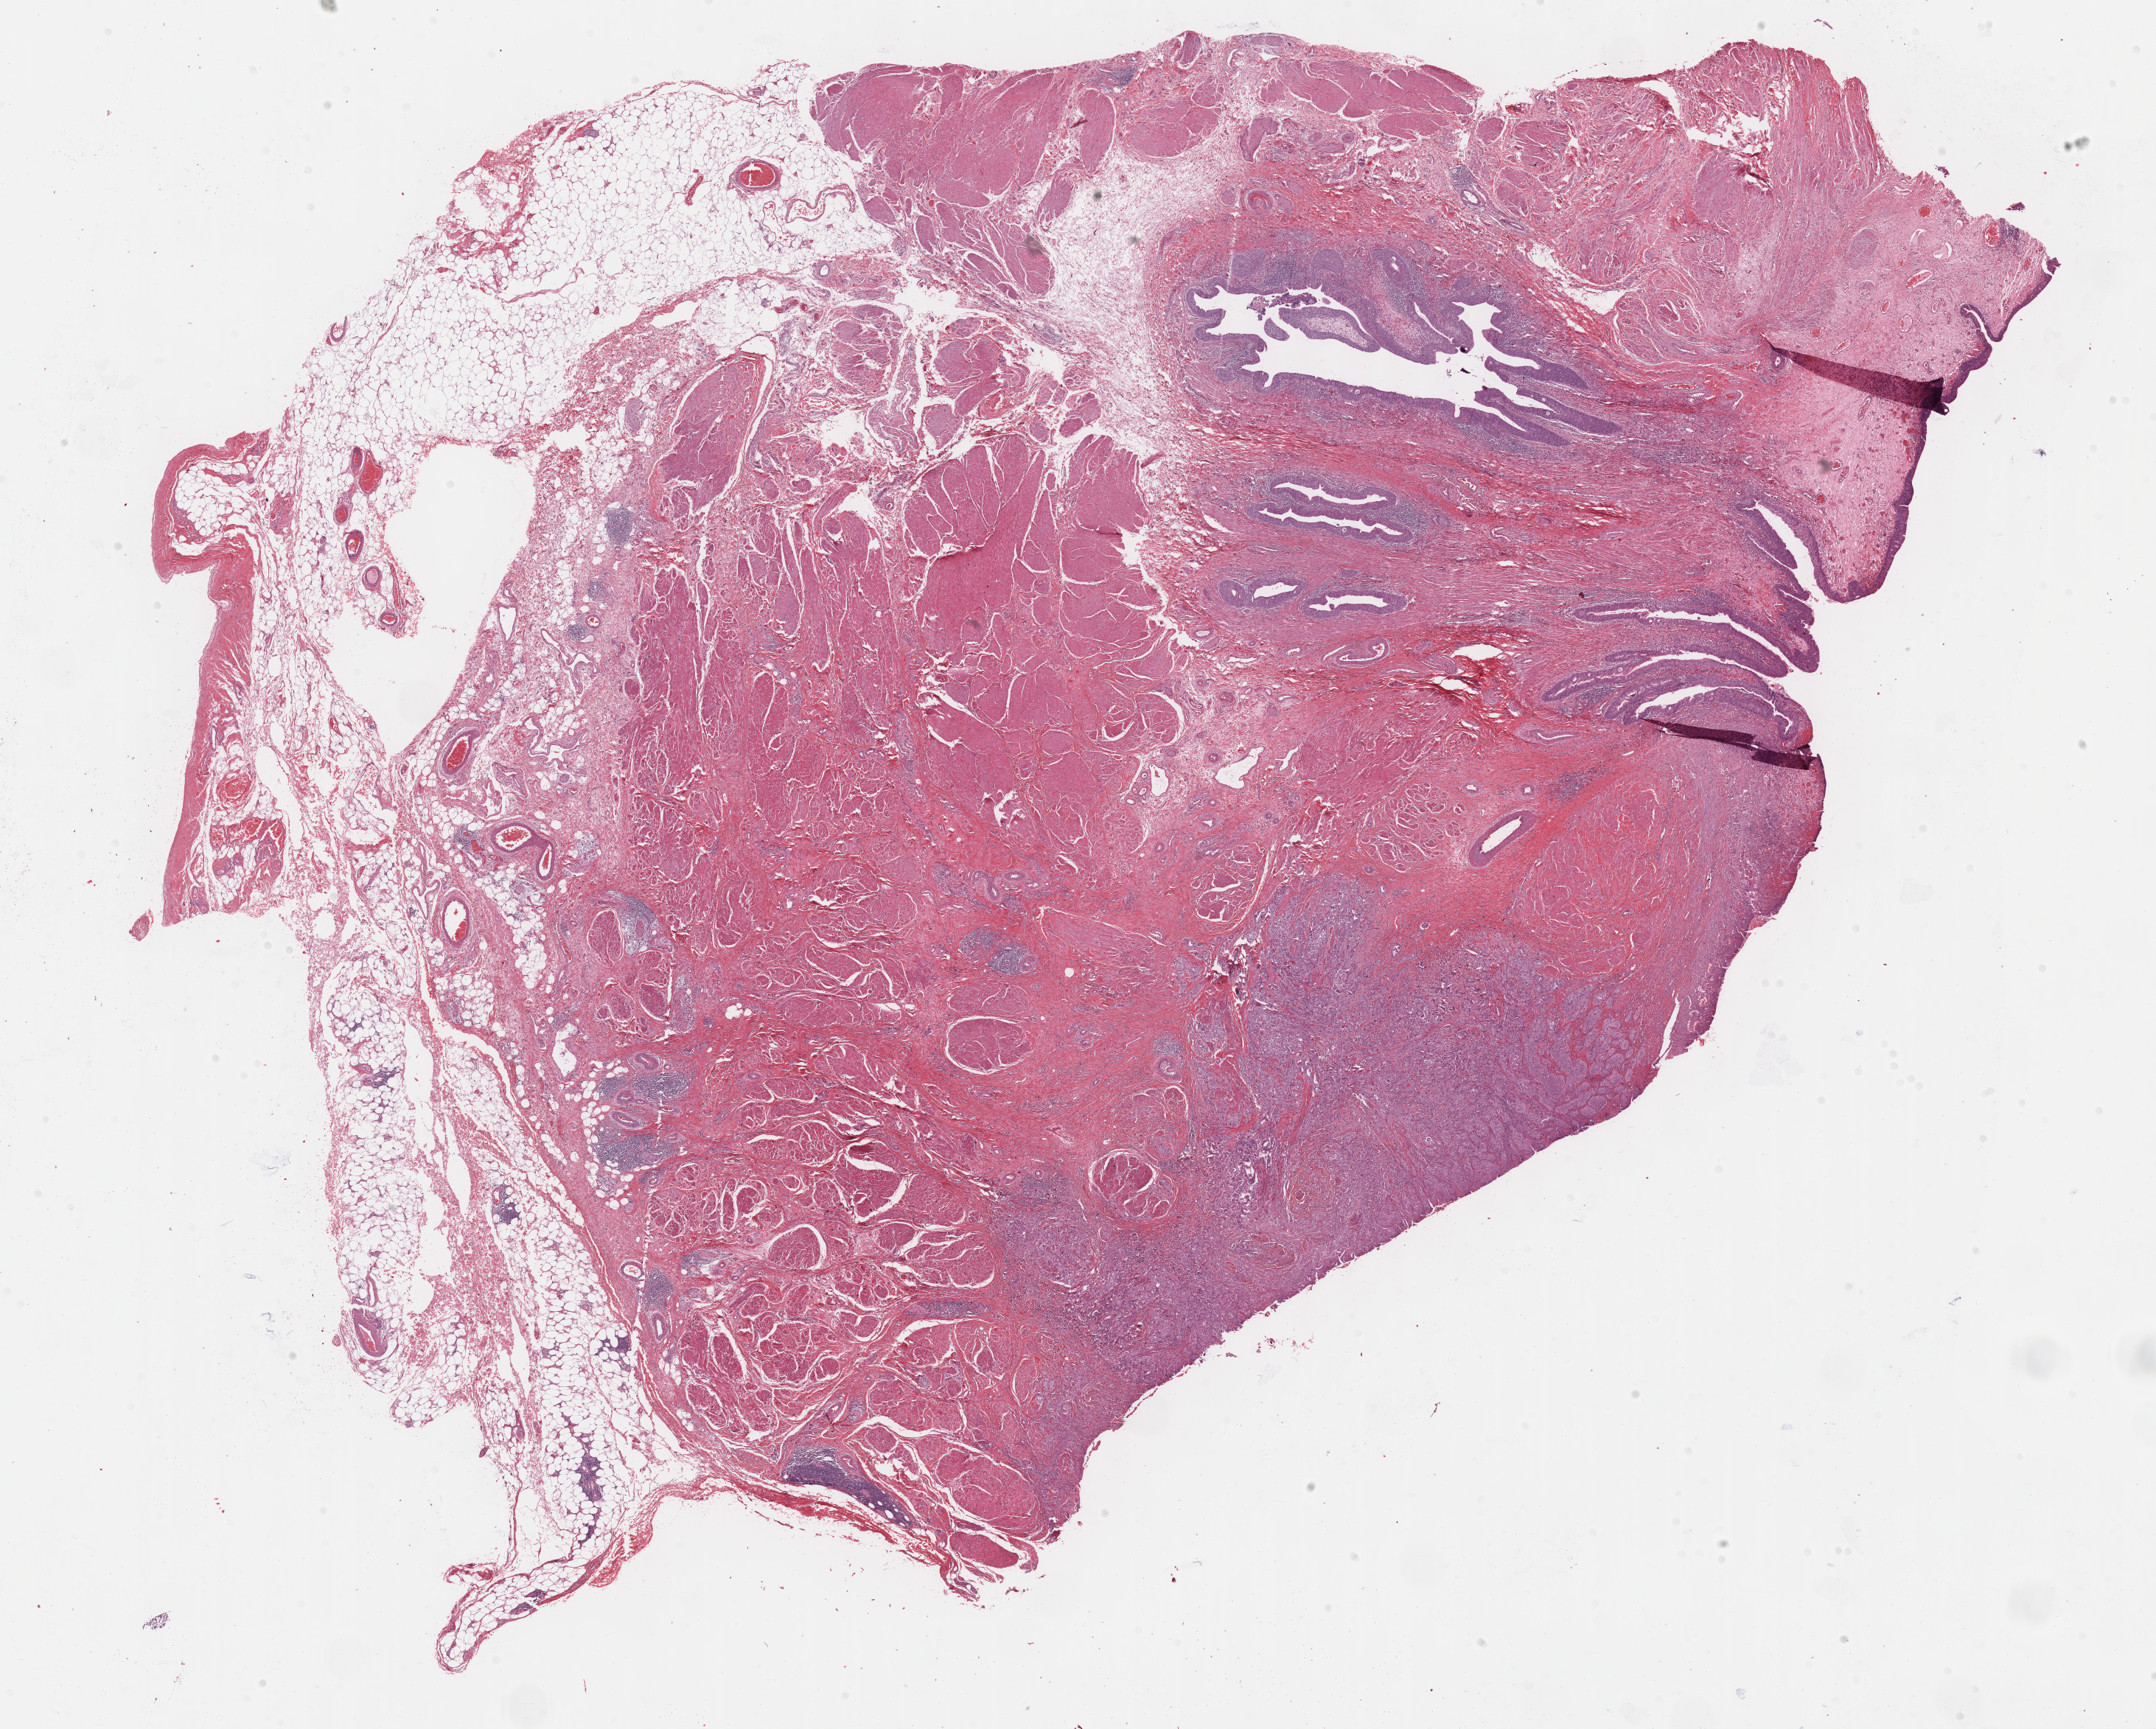
H&E-stained whole-slide image — shown as a low-resolution overview of the whole scanned area (about 23.7 x 19.0 mm, slide scanned at 40x); formalin-fixed paraffin-embedded (FFPE) diagnostic section; bladder, primary tumour sample. Patient: male, age at initial diagnosis 85 years. Histologic grade: high grade.
- histologic diagnosis: Transitional cell carcinoma
- lymph nodes positive (case pathology): 4 of 19 examined
- AJCC pathologic stage: IV (6th edition)